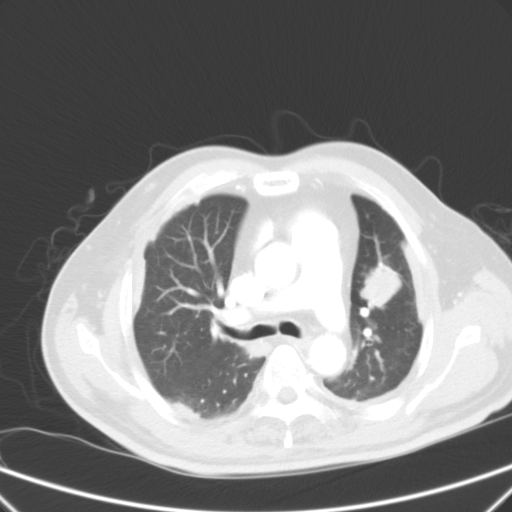
Chest CT, one axial slice. Position 39 of 59 along the scan axis. Intravenous contrast given. Lung window (W 1500 / L -600 HU). 5 mm slice thickness. 512 × 512 image matrix, field of view 357 × 357 mm. Male patient, age 66 years. From the clinical record (not read from this slice): clinical TNM (as recorded): T1c N3 M1a.
Structures marked on this image (rectangle marked by the reading radiologist):
- lung tumour (recorded histology: squamous cell carcinoma): bounding box (x1, y1, x2, y2) in pixels: (356, 260, 408, 315)